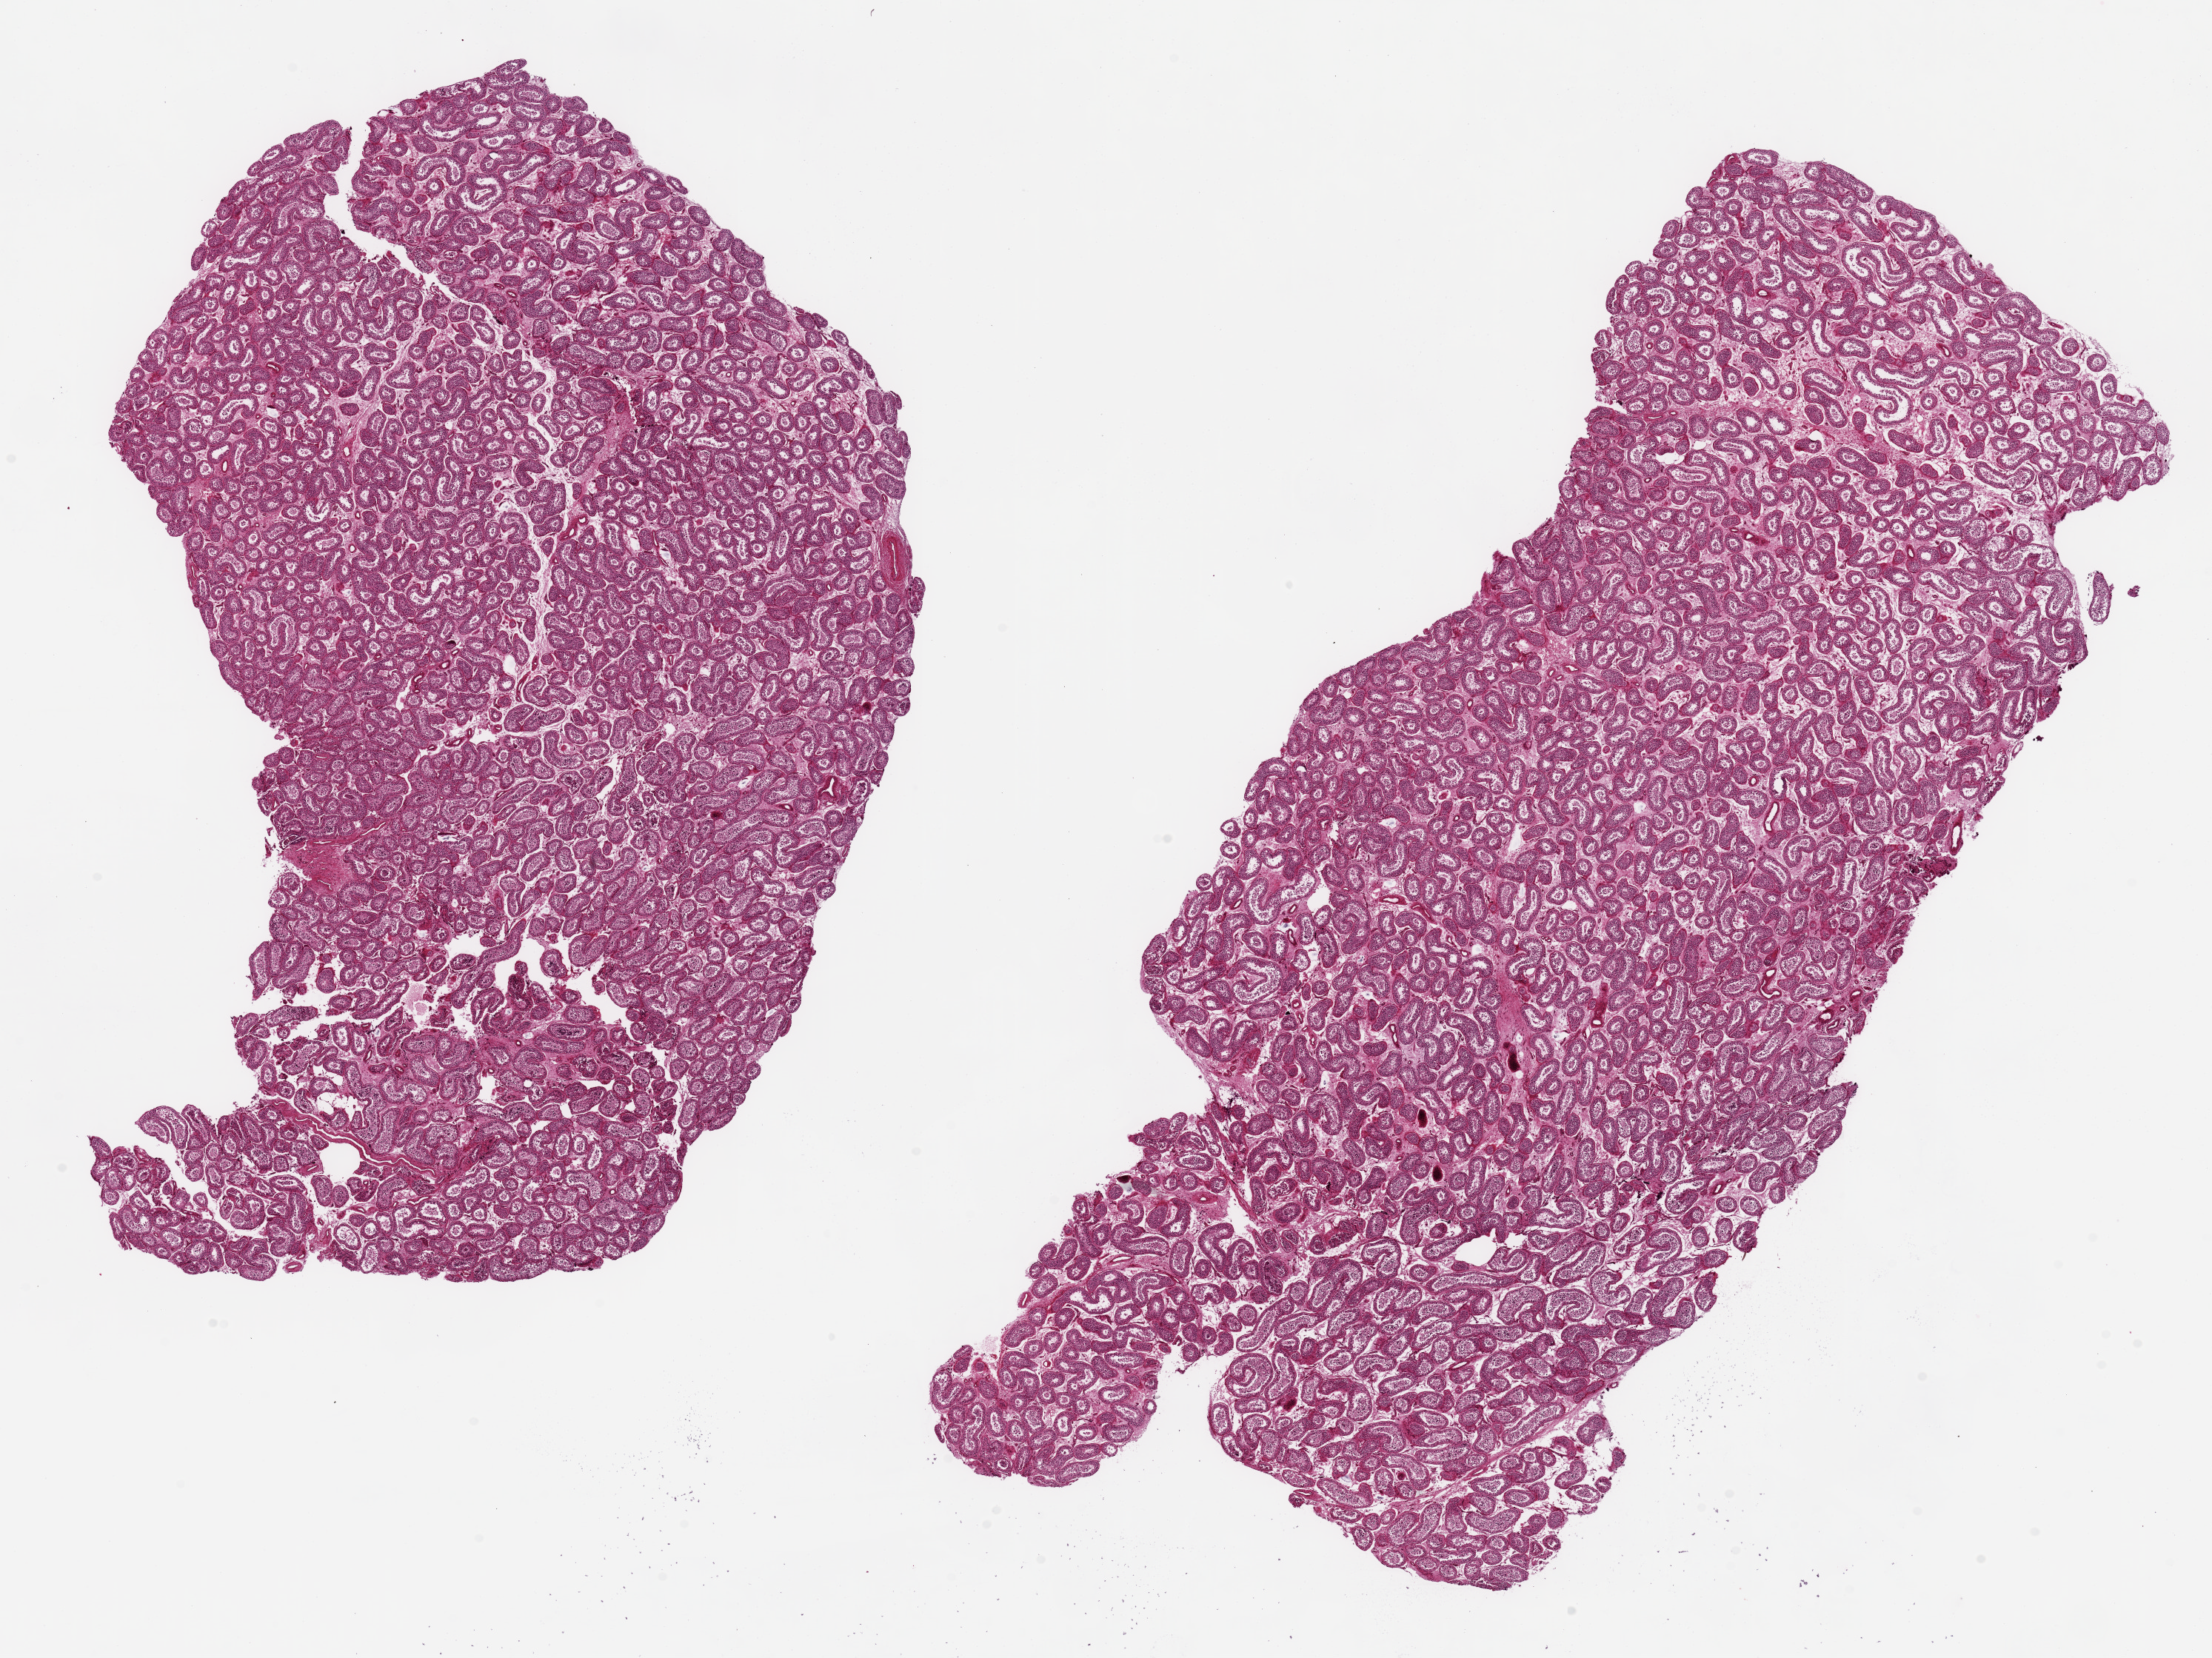
Whole-slide image, hematoxylin and eosin (H&E) stain, whole scanned area (about 23.6 x 17.7 mm, slide scanned at 20x) shown as a low-resolution overview. PAXgene-fixed, paraffin-embedded tissue. Sampled site (target tissue): testis. Donor tissue sample. Donor sex: male.
Reviewer comment on this tissue sample: 2 pieces 14x7 & 9x12 mm; spermatogenesis present.